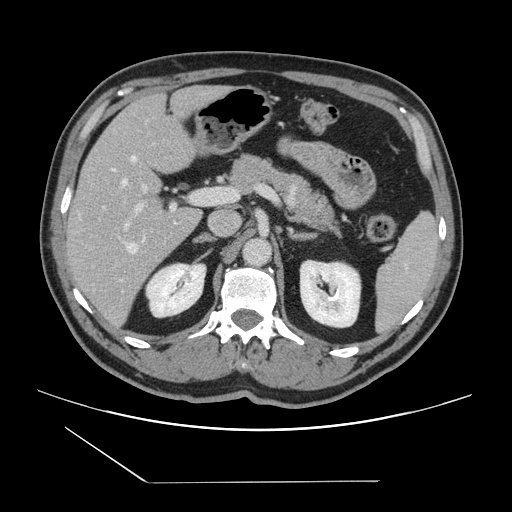
Contrast-enhanced abdominal CT, one axial slice. Slice 81 of 157 in the series (ordered by position). Intravenous contrast given. Soft-tissue window (W 400 / L 40 HU). 512 × 512 image matrix, field of view 407 × 407 mm. Male patient, age 61 years. Case-level facts recorded for this patient, not image findings: diagnosis: colorectal cancer liver metastases, imaged before liver resection; multiple liver metastases: yes; largest metastasis: 5.5 cm; disease in both lobes: yes.
Annotated regions visible in this slice (outlined manually by an expert reader):
- hepatic veins: bounding box <113,156,144,281> (left, top, right, bottom; pixels)
- liver: <68,85,225,331>
- planned liver remnant (the part of the liver to remain after resection): <68,86,223,221>
- portal vein (with intrahepatic branches): <104,186,206,229>